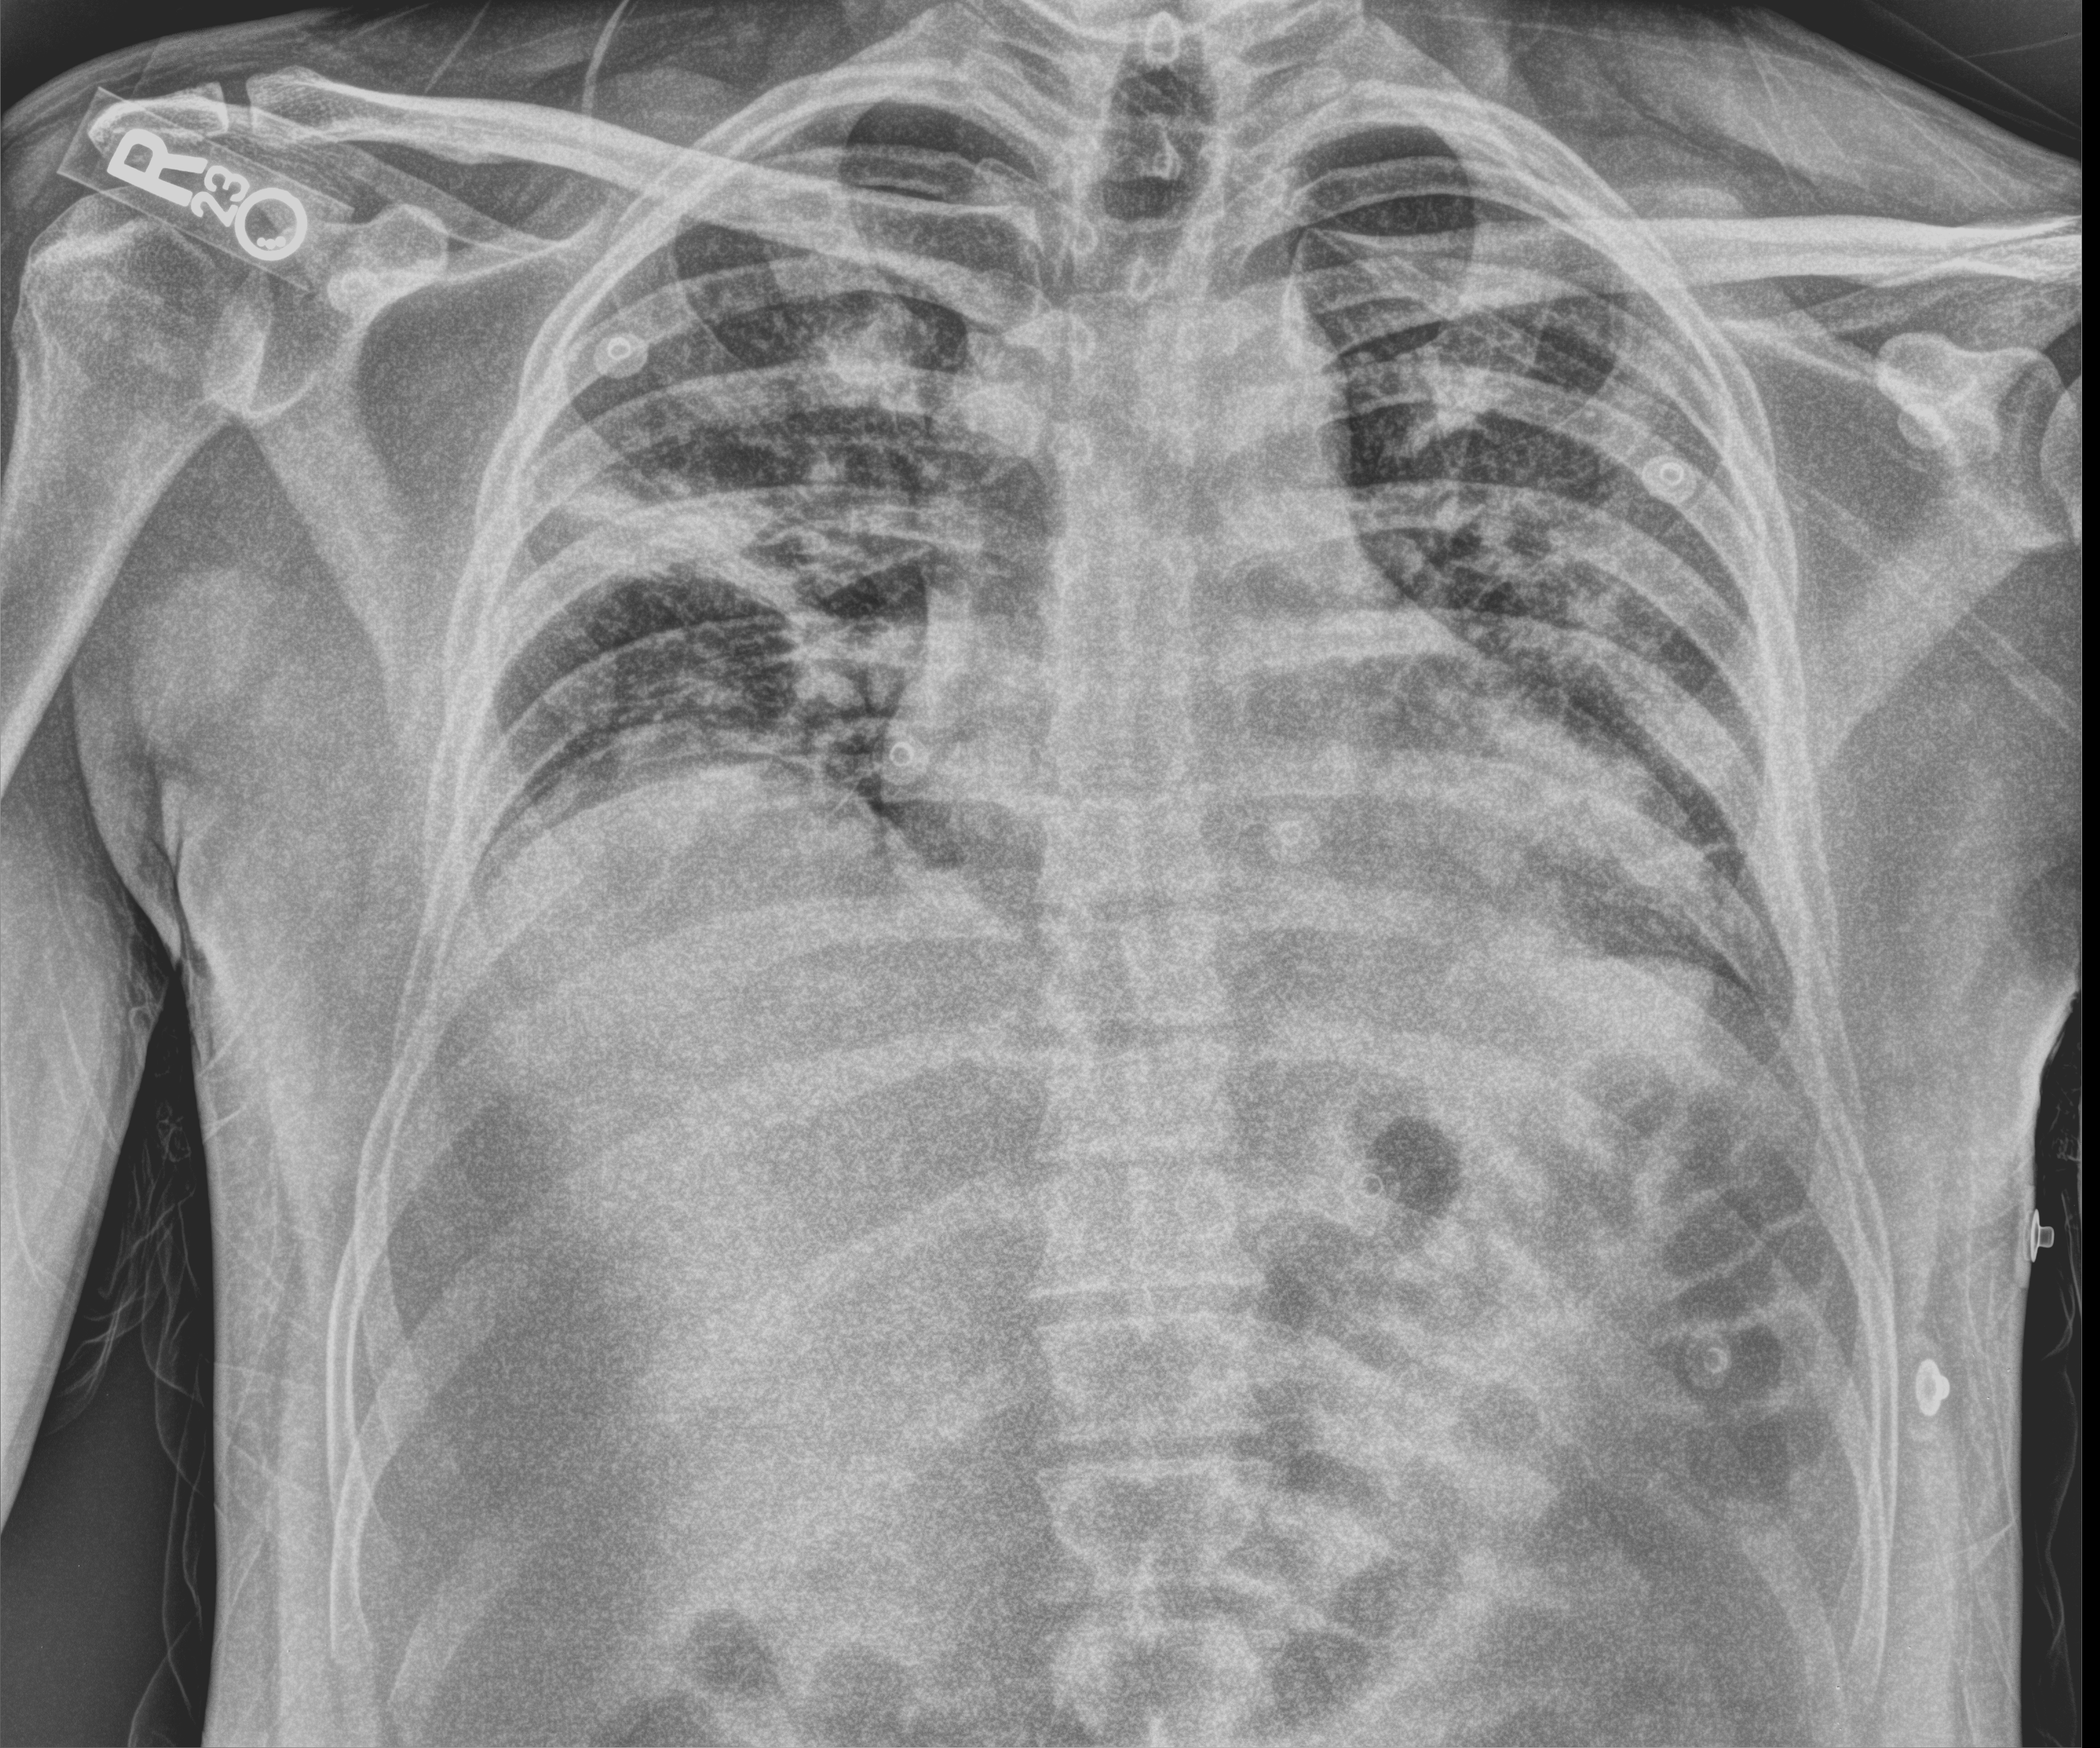
Bedside chest radiograph (computed radiography); anteroposterior (AP) projection. Male patient hospitalised with COVID-19, age 18–59 years.
Hospital-stay facts (about this admission, not read from this image; timing relative to this image not recorded):
- admitted to intensive care during this hospital stay: no